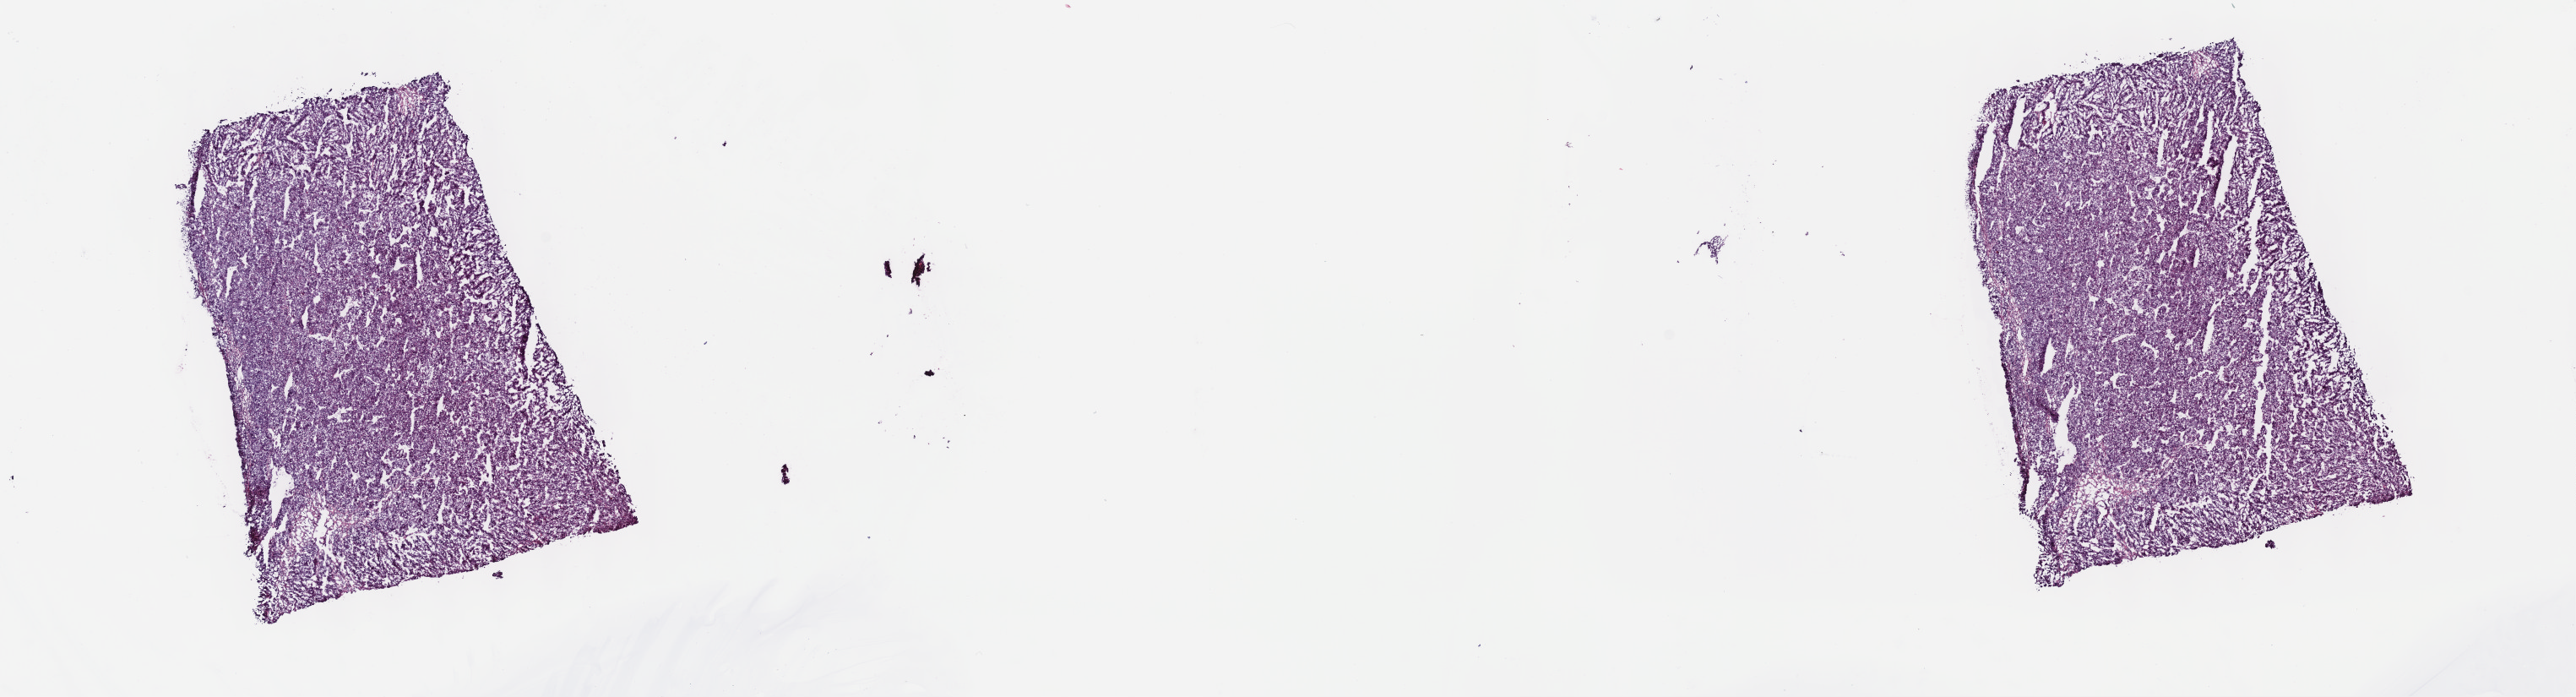
Digitized Hematoxylin and eosin (H&E) stained tissue section (whole slide), a low-resolution overview of the entire scanned area, about 24.7 x 6.7 mm, frozen section, liver, primary tumour sample. Male patient; age at initial diagnosis 74 years. Histologic grade: G2 (moderately differentiated). Slide review estimates, as recorded: tumour cells 100%, tumour nuclei 95%, normal cells 0%, stromal cells 0%, necrosis 0%. Infiltration values recorded for this section: lymphocyte infiltration 0%, monocyte infiltration 0%, neutrophil infiltration 0%.
AJCC pathologic stage: IIIA. Histologic diagnosis: Hepatocellular carcinoma, NOS. TNM: T3 N0 M0.